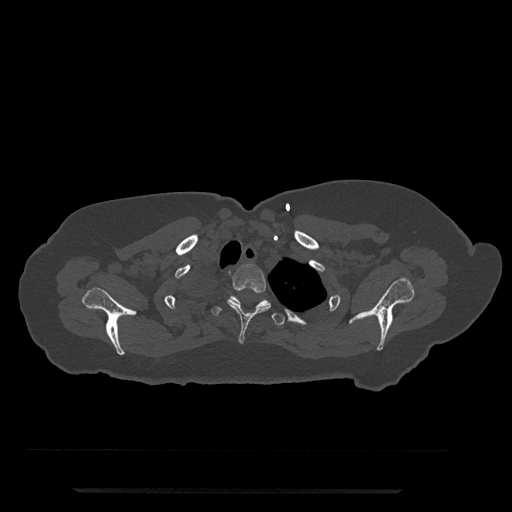
CT including the spine, one axial slice; position 662 of 797 along the scan axis; reconstruction kernel Br40s/3; 120 kVp; bone window (W 1800 / L 400 HU); 0.5 mm slice thickness; 512 × 512 image matrix, field of view 440 × 440 mm. Patient: female, 51 years. From the clinical record (not read from this slice): primary cancer: neuro; vertebrae with lytic lesions (as recorded): T8.
Annotated regions visible in this slice (semi-automatically segmented with operator editing):
- T2 vertebra: bounding box (x1, y1, x2, y2) in pixels: (227, 263, 271, 344)
- T3 vertebra: (211, 295, 285, 326)